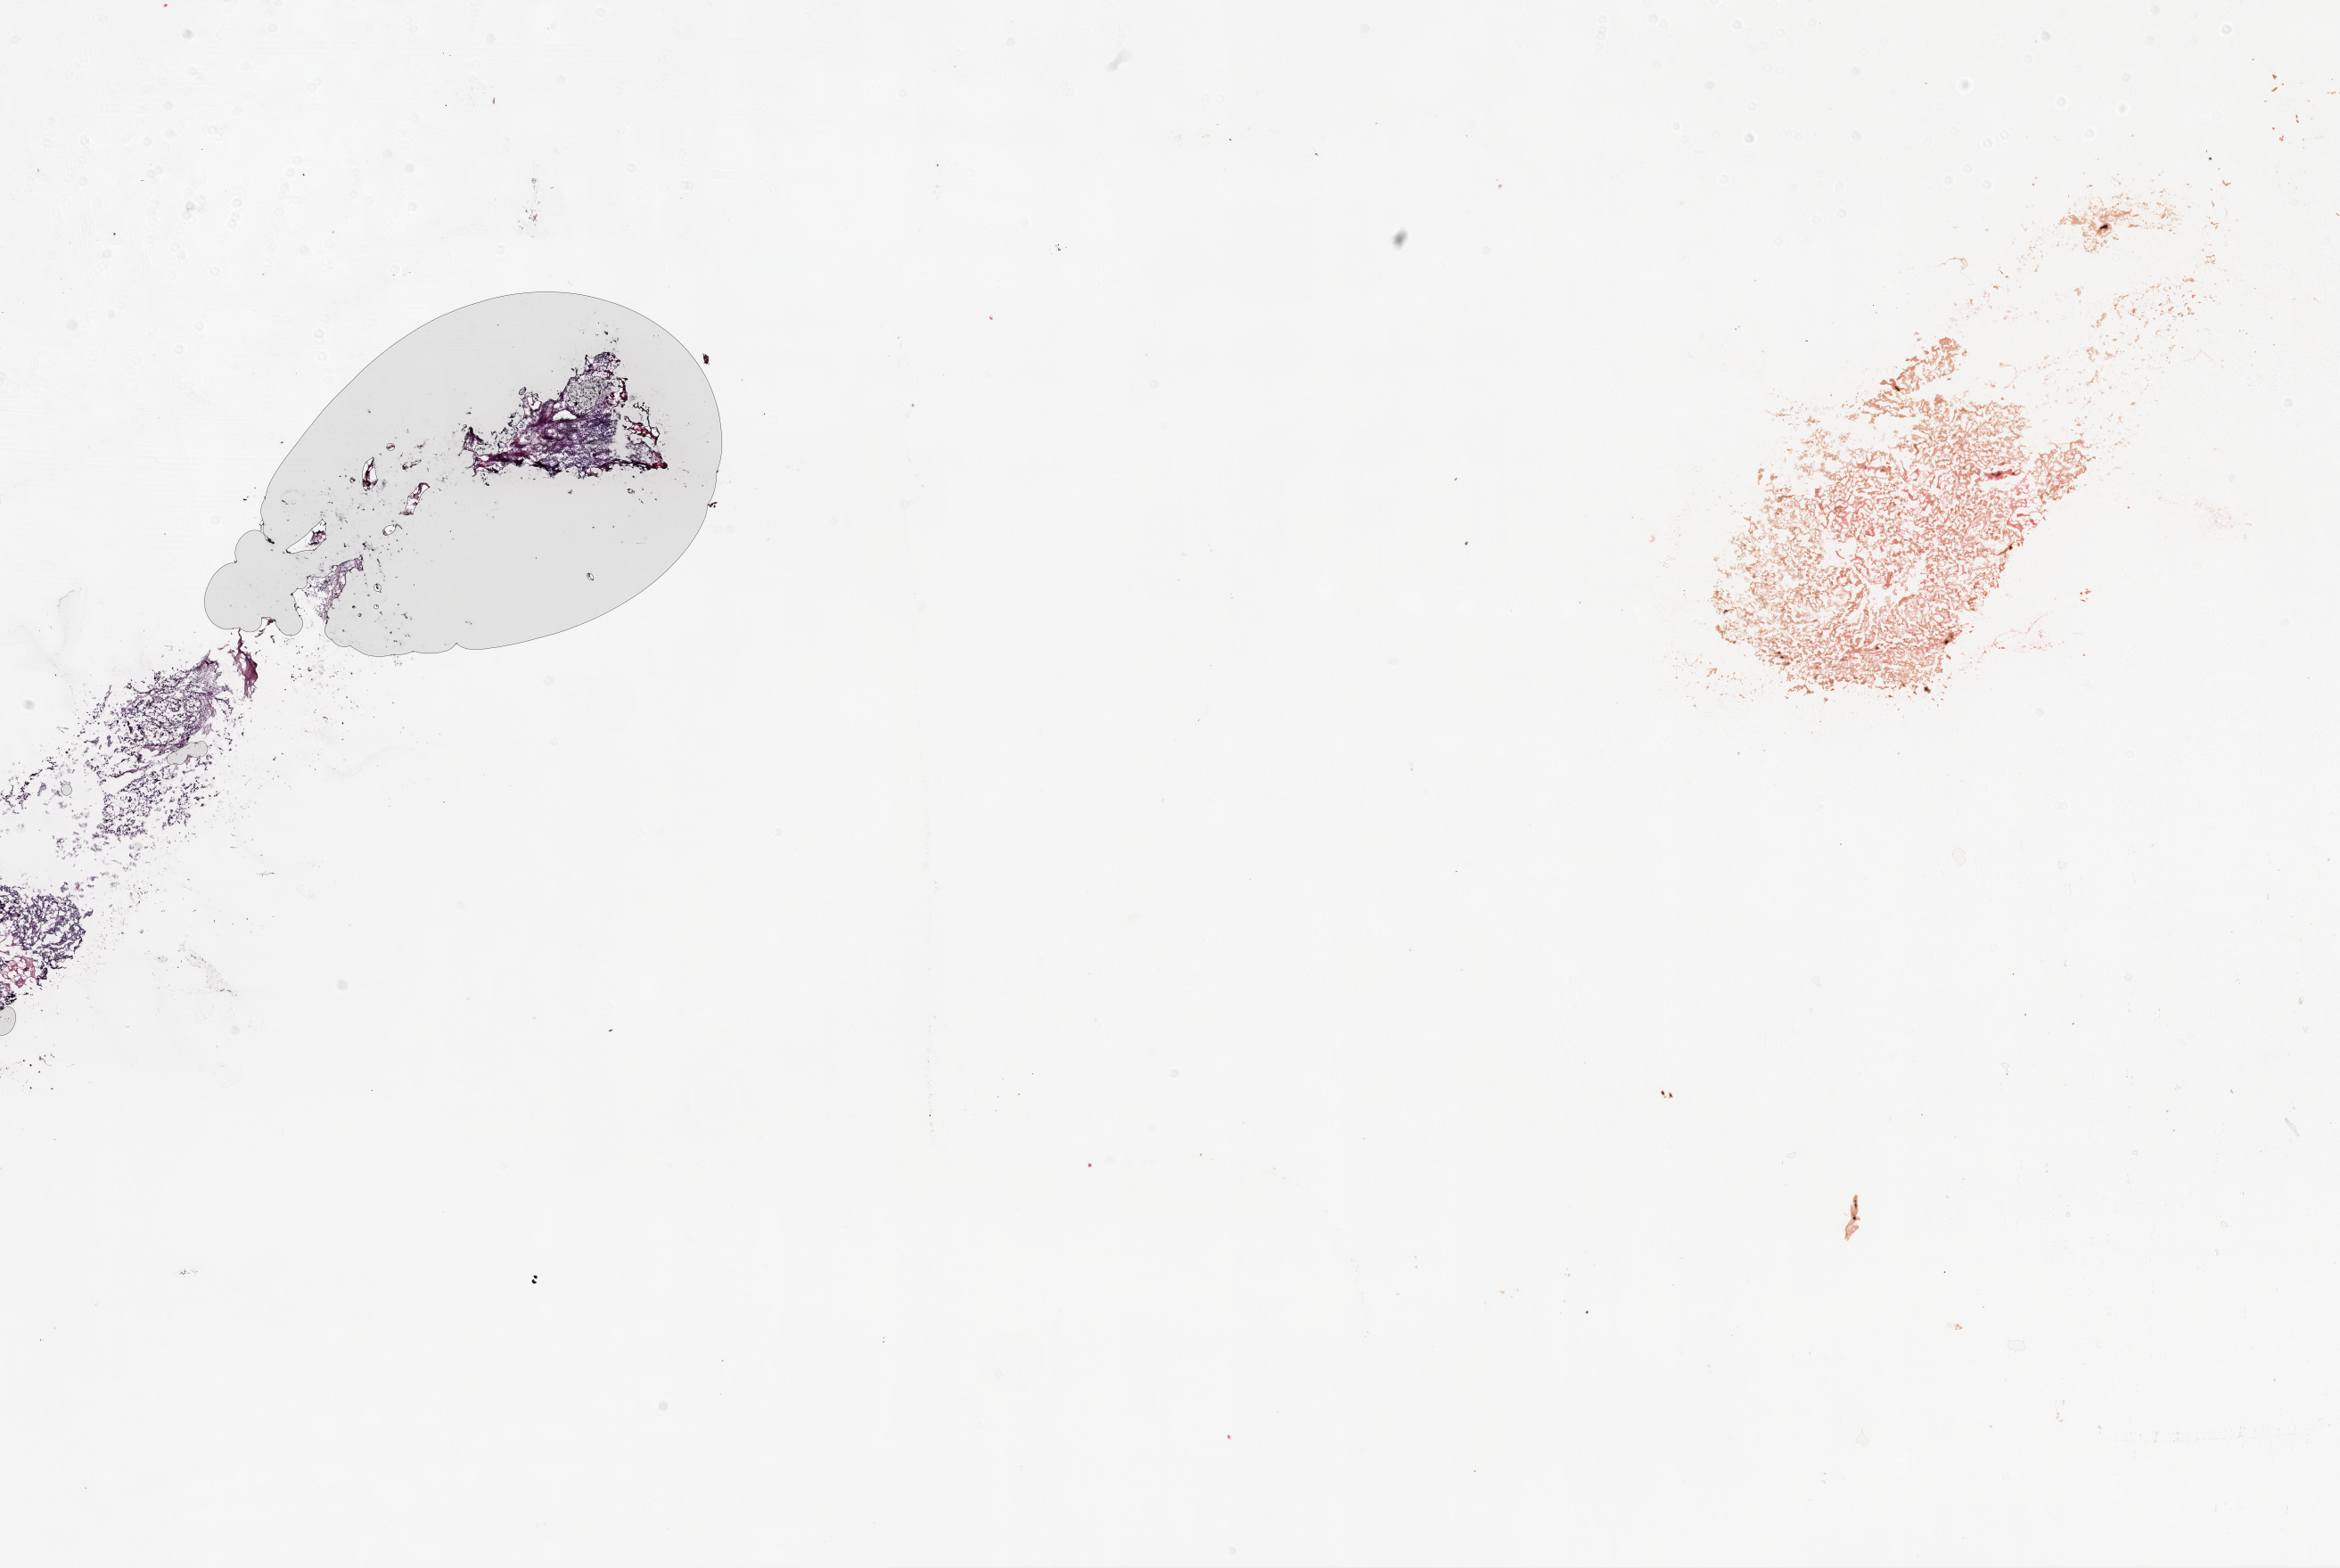
H&E-stained whole-slide image — a low-resolution overview of the entire scanned area, about 21.1 x 14.1 mm (slide scanned at 20x). Frozen section. Sample: primary tumour, ovary. Patient: female, age at initial diagnosis 50 years. Histologic grade: G3 (poorly differentiated). Composition of this section per pathologist review: tumour nuclei 0%, necrosis 0%.
• FIGO stage: IV
• diagnosis: Serous cystadenocarcinoma, NOS